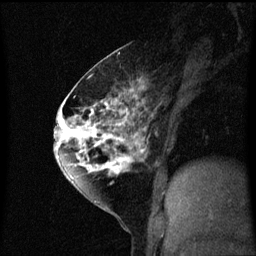
Breast MRI (dynamic contrast-enhanced), one sagittal slice; slice 31 of 60 in the series (ordered by position); dynamic contrast-enhanced series, image 2 of 3 at this slice position (ordered by acquisition); 1.5 T; TE 4.2 ms, TR 8.4 ms; 2 mm slice thickness; 256 × 256 image matrix, field of view 200 × 200 mm. Female patient, age 60 years.
Outlined on this slice (semi-automatic segmentation, software-assisted and operator-edited):
- analysis volume of interest (the breast-tissue region the enhancement analysis was run in; not a lesion): bounding box [x1, y1, x2, y2] px = [64, 70, 143, 195]
- tumour enhancement mask (voxels above the 70 % enhancement threshold inside the analysis volume of interest): [64, 76, 143, 189]